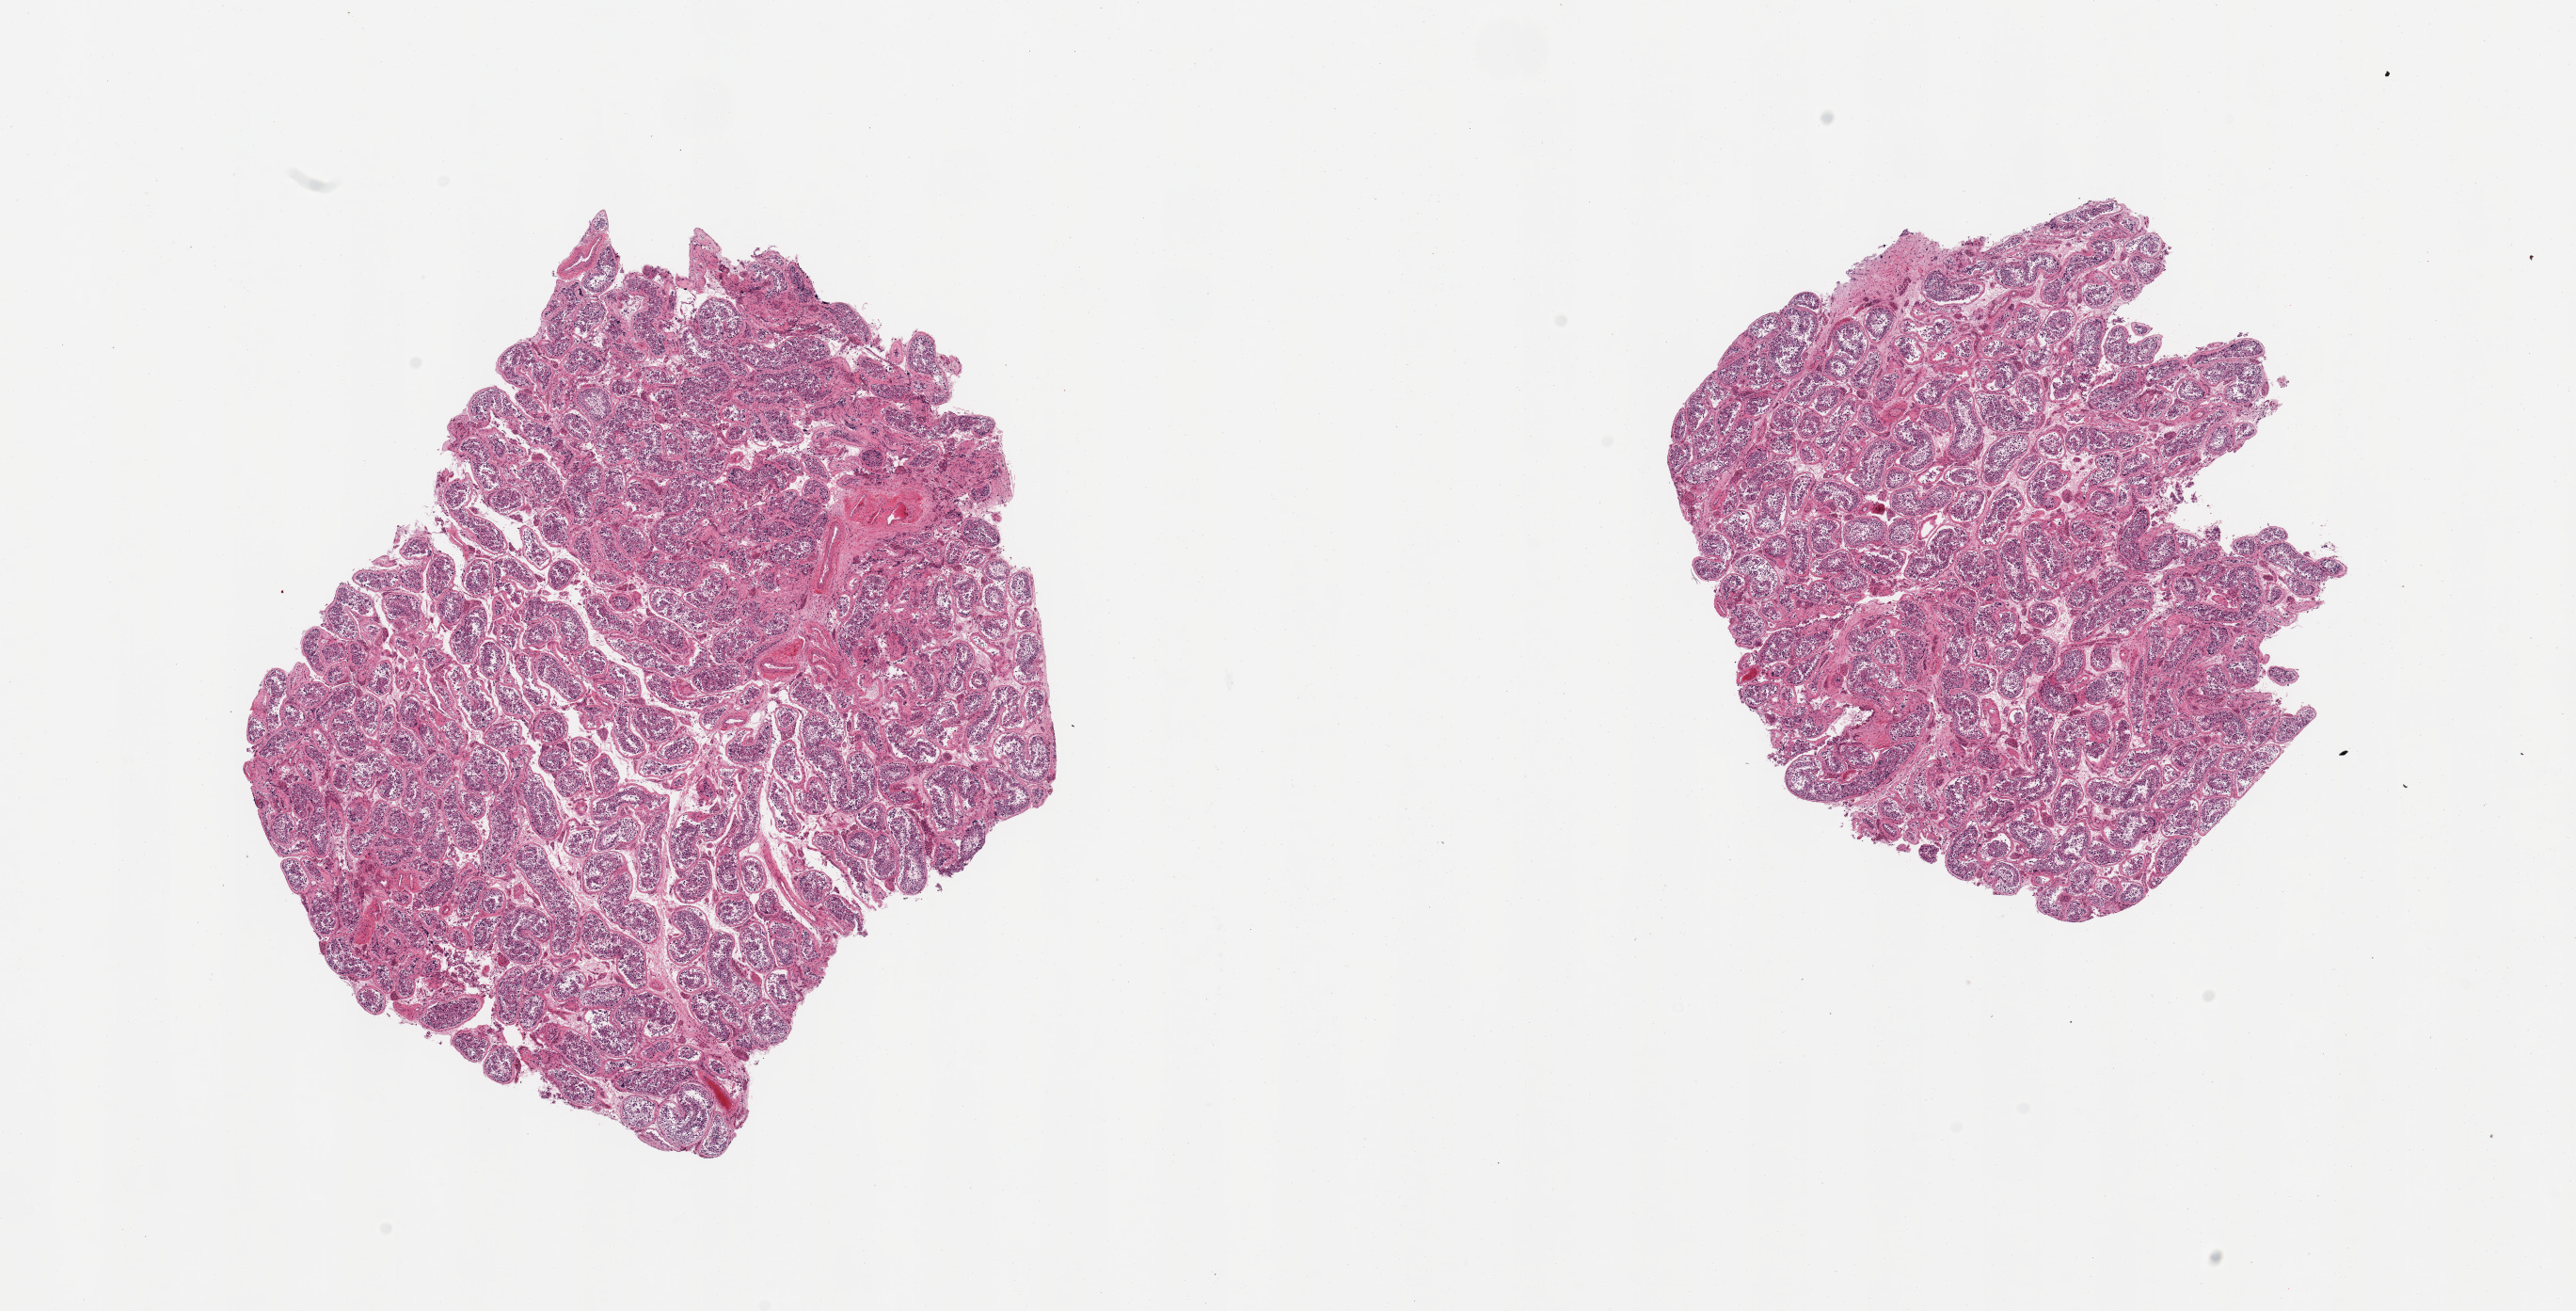
Digitized hematoxylin and eosin (H&E)-stained section, low-resolution overview of the scanned area, about 21.7 x 11.0 mm (from a 20x scan). PAXgene-fixed, paraffin-embedded tissue. Target tissue: testis. Tissue donor sample. Donor: male.
Reviewer comment on this tissue sample: 2 pieces; spermatogenesis present.